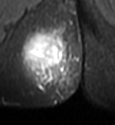
MRI of an extremity soft-tissue mass, one axial slice. Slice 17 of 49 in the series (ordered by position). STIR. MR volume resampled by the dataset authors to the PET/CT grid (not the native acquisition matrix). 3.27 mm slice thickness. 115 × 125 image matrix. Female patient. Case-level facts recorded for this patient, not image findings: histological type: epithelioid sarcoma; grade: intermediate; site of the primary tumour: right buttock.
Structures marked on this image (expert contour drawn on MRI and transferred to this co-registered scan by the dataset authors):
- gross tumour volume including surrounding oedema: bounding box <20,25,78,97> (left, top, right, bottom; pixels)
- gross tumour volume (mass): <24,32,66,72>